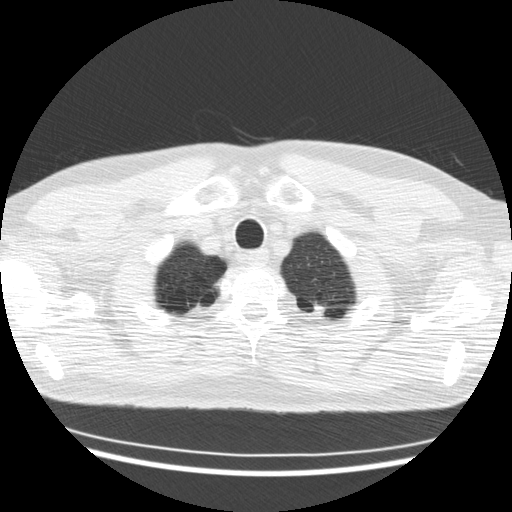
Chest CT (low-dose screening protocol), one axial image; second screening round (one year after baseline); lung window (W 1500 / L -600 HU); standard (soft-tissue) reconstruction kernel (STANDARD); 512 × 512 image matrix. Male participant, aged 57 years at enrolment. Former smoker at enrolment.
Lesion marked by an expert reader, box from (x=304, y=298) to (x=333, y=323) px. The screening reader recorded 2 non-calcified nodules or masses ≥4 mm on this exam; which of them this box marks is not recorded.